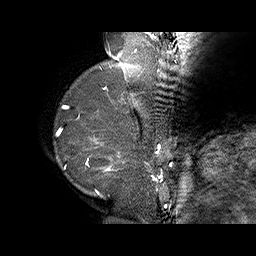
Breast MRI (dynamic contrast-enhanced), one sagittal slice; slice 8 of 70 in the series (ordered by position); dynamic contrast-enhanced series, time point 2 of 6 at this slice position (early post-contrast); 1.5 T; TE 4.5 ms, TR 32.4 ms; 3 mm slice thickness; 256 × 256 image matrix, field of view 180 × 180 mm. Female patient. Case-level facts recorded for this patient, not image findings: setting: breast cancer imaged before/during neoadjuvant chemotherapy; receptor status: HR-positive, HER2-negative.
Structures marked on this image (semi-automatic segmentation, software-assisted and operator-edited):
- analysis volume of interest (the breast-tissue region the enhancement analysis was run in; not a lesion): box from (x=71, y=128) to (x=159, y=202) px
- tumour enhancement mask (voxels above the 100 % enhancement threshold inside the analysis volume of interest): (x=86, y=137)–(x=159, y=194)